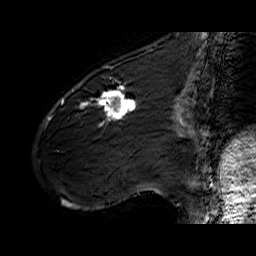
Breast MRI (dynamic contrast-enhanced), one sagittal slice. Slice 19 of 60 in the series (ordered by position). Dynamic contrast-enhanced series, time point 2 of 6 at this slice position (early post-contrast). 1.5 T. TE 6.4 ms, TR 32.9 ms. 4 mm slice thickness. 256 × 256 image matrix, field of view 200 × 200 mm. Female patient. From the clinical record (not read from this slice): setting: breast cancer imaged before/during neoadjuvant chemotherapy; receptor status: HER2-positive.
Outlined on this slice (semi-automatic segmentation, software-assisted and operator-edited):
- analysis volume of interest (the breast-tissue region the enhancement analysis was run in; not a lesion): bounding box <61,77,141,142> (left, top, right, bottom; pixels)
- tumour enhancement mask (voxels above the 100 % enhancement threshold inside the analysis volume of interest): <62,87,138,126>